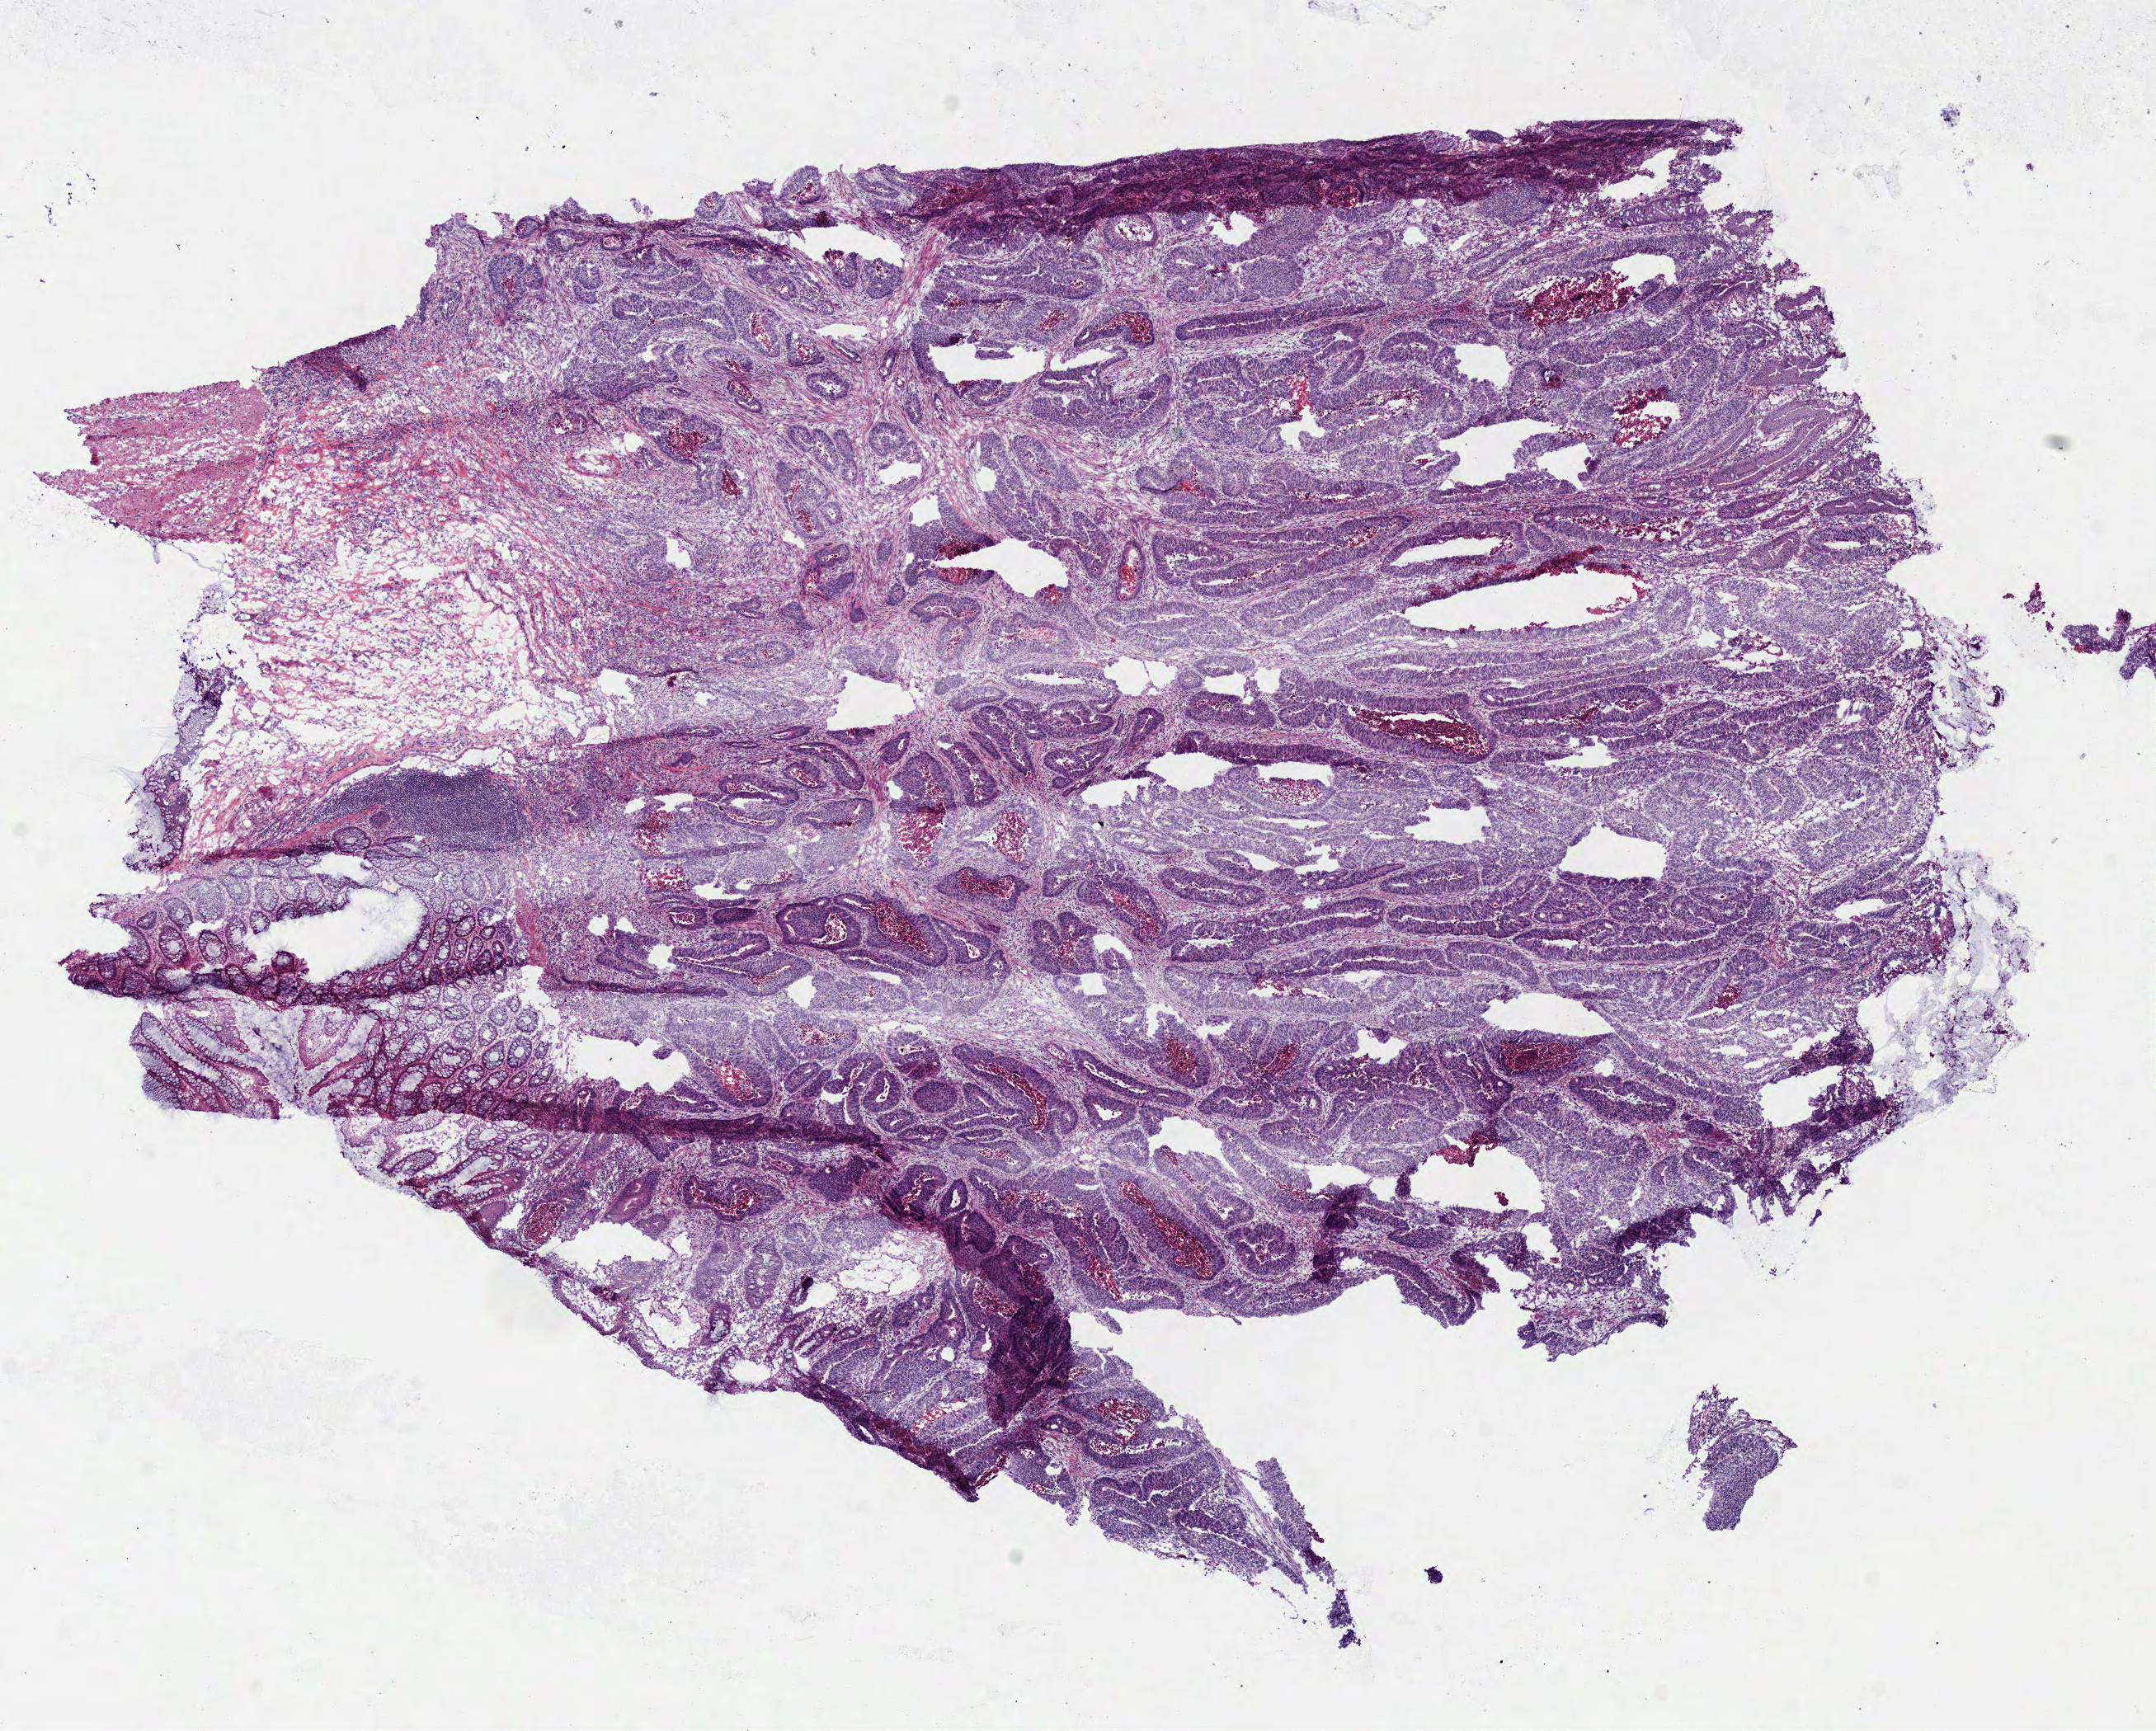
H&E-stained whole-slide image, whole scanned area (about 10.3 x 8.3 mm) shown as a low-resolution overview, frozen section, sample: primary tumour, rectum. Female, age 78 years at initial diagnosis. Slide review estimates, as recorded: tumour cells 75%, tumour nuclei 75%, normal cells 5%, stromal cells 15%, necrosis 5%.
AJCC pathologic stage: IIA (7th edition). Pathologic diagnosis: Tubular adenocarcinoma.